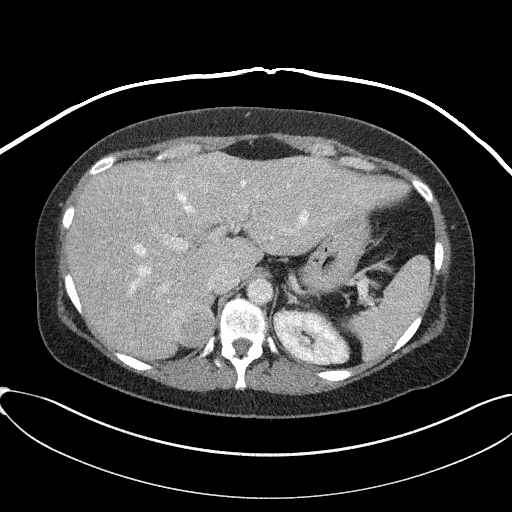
Contrast-enhanced abdominal CT, one axial slice; intravenous contrast given; soft-tissue window (W 400 / L 40 HU); 3 mm slice thickness; 512 × 512 image matrix, field of view 410 × 410 mm. Patient: female, 46 years. From the clinical record (not read from this slice): diagnosis: adrenocortical carcinoma; tumour side: right adrenal; tumour size at pathology: 7.2 cm; Ki-67 index: 50 %; stage (as recorded): 4.
Structures marked on this image (semi-automatically segmented with operator editing):
- mass: bounding box <171,300,213,345> (left, top, right, bottom; pixels)